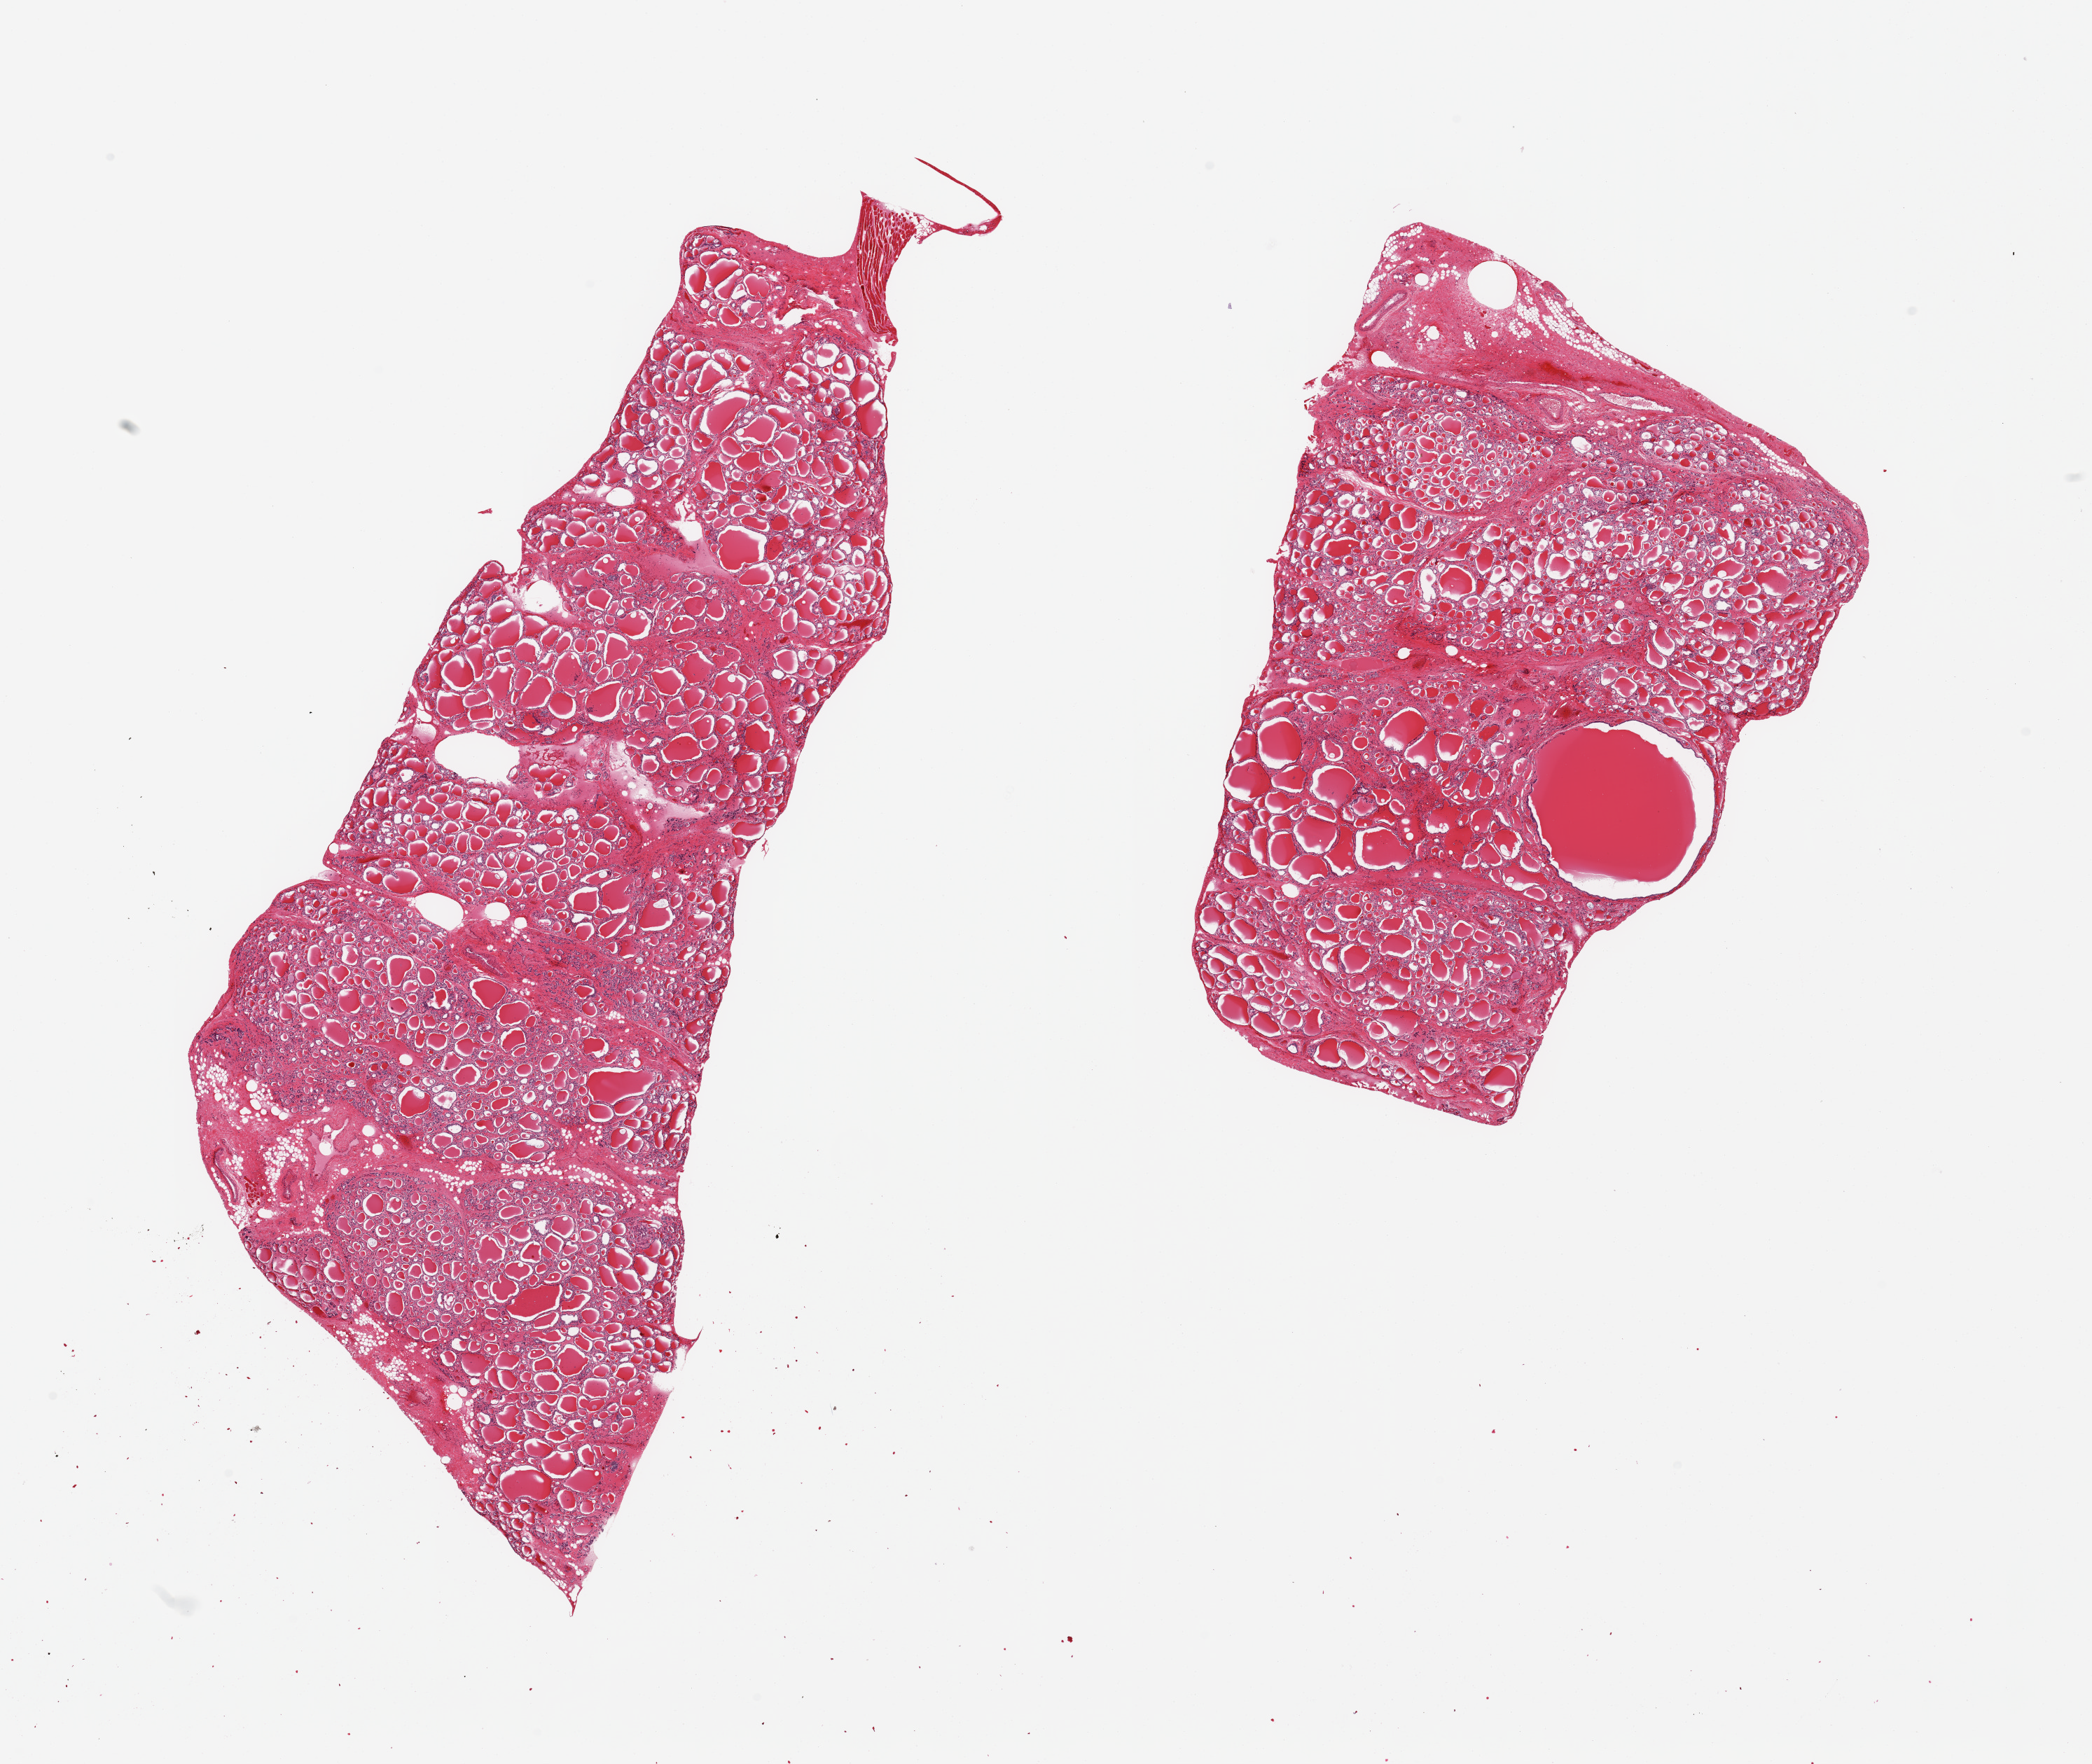
Digitized haematoxylin and eosin-stained section — low-resolution overview of the scanned area, about 23.6 x 19.9 mm. PAXgene-fixed, paraffin-embedded tissue. Target tissue: thyroid. Donor tissue sample. Donor: female.
Review note (as recorded): 2 pieces; small attachments of fat/skeletal muscle (up to 10%), nodular hyperplasia.